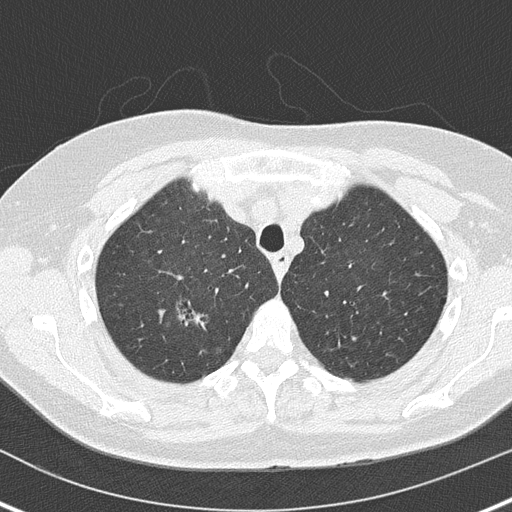
Chest CT (low-dose screening protocol), one axial image, baseline annual screen, lung window (W 1500 / L -600 HU), 2 mm slice thickness, lung (sharp) reconstruction kernel (B50f), slice 33 of 162 in the series. Female, age 61 years at enrolment. Current smoker at enrolment.
Lesion marked by an expert reader, bounding box [x1, y1, x2, y2] px = [182, 302, 218, 333]. Reader record for this screening exam (exam-level; its link to the box is not recorded): non-calcified nodule or mass ≥4 mm, right upper lobe, 8 × 5 mm, smooth margins, soft tissue attenuation. Official screen result: positive, change unspecified: nodule(s) >= 4 mm or enlarging nodule(s), mass(es), or other non-specific abnormalities suspicious for lung cancer. Lung cancer was diagnosed 438 days after this screen: adenocarcinoma, NOS, right upper lobe, moderately differentiated (G2), stage IA (AJCC 6th edition), 20 mm at pathology.